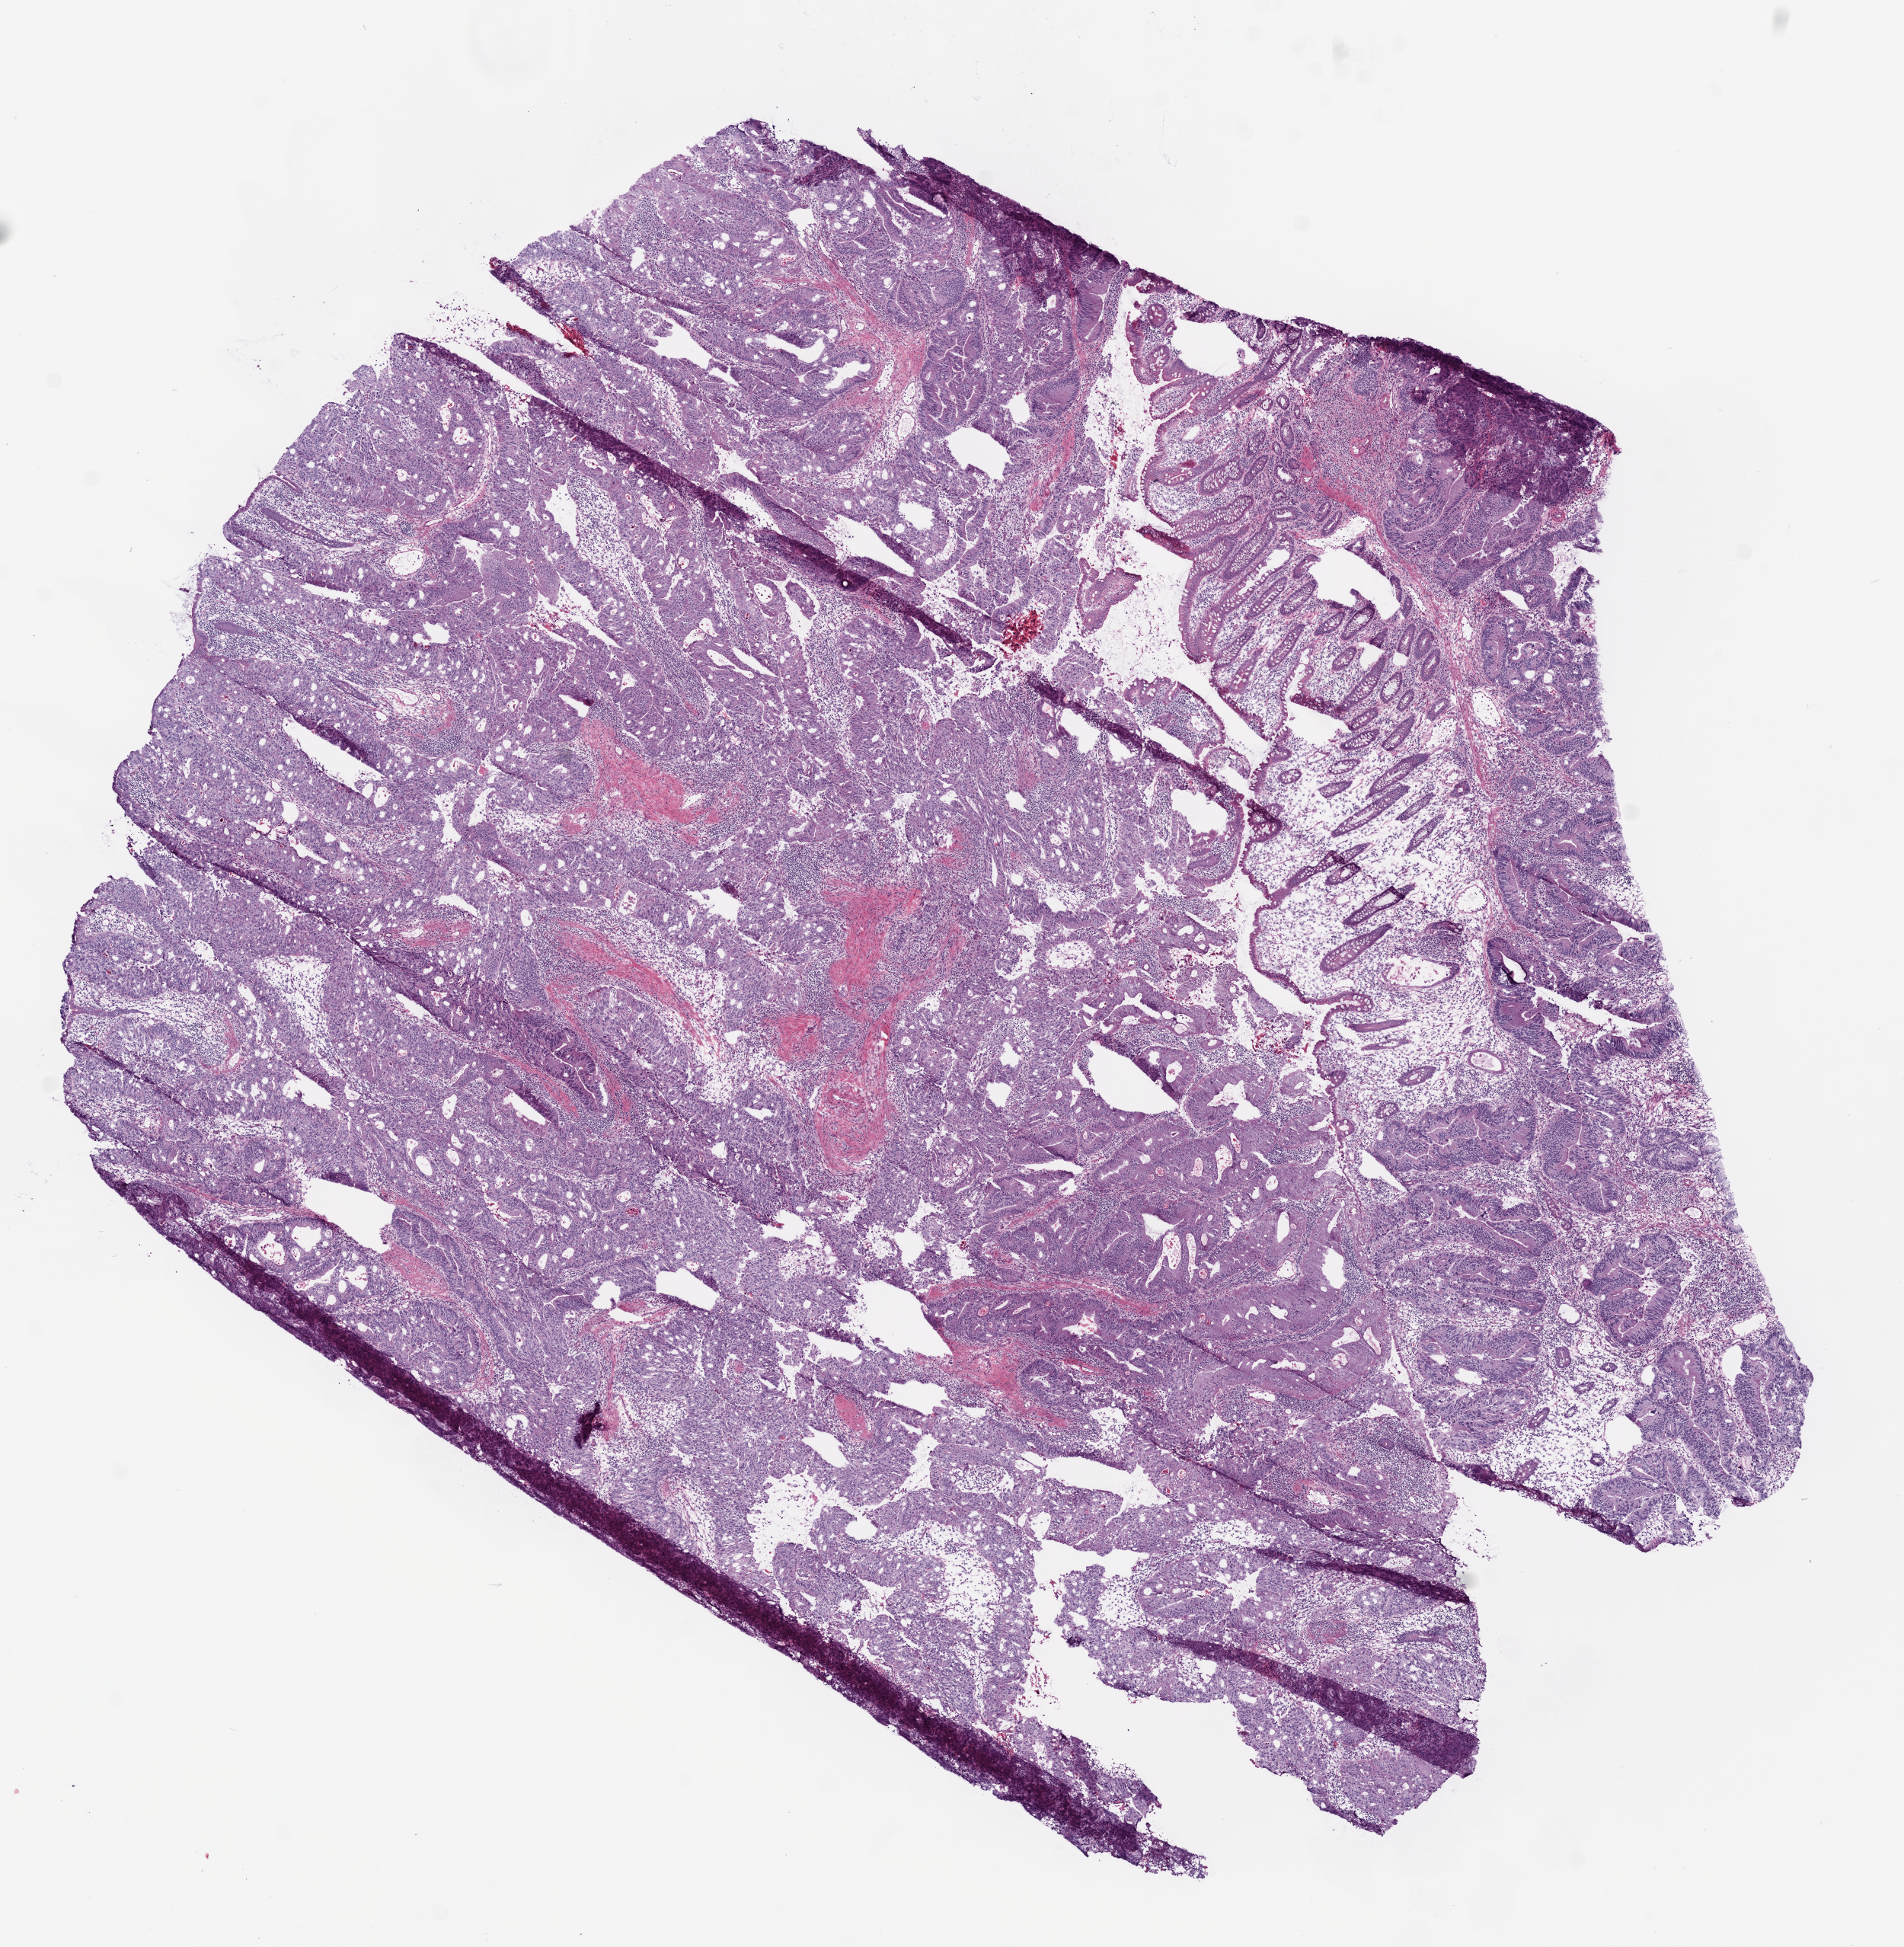
Whole-slide histology image, Hematoxylin and eosin (H&E) stained — a low-resolution overview of the entire scanned area, about 10.0 x 10.3 mm (slide scanned at 20x), frozen section from the bottom of the tissue portion, colon, primary tumour sample. Male, age 85 years at initial diagnosis. Slide review estimates, as recorded: tumour cells 90%, tumour nuclei 90%, normal cells 5%, stromal cells 5%, necrosis 0%.
- lymph nodes positive (case pathology): 10 of 20 examined
- AJCC pathologic stage: IIIC (6th edition)
- histologic diagnosis: Adenocarcinoma, NOS (cecum)